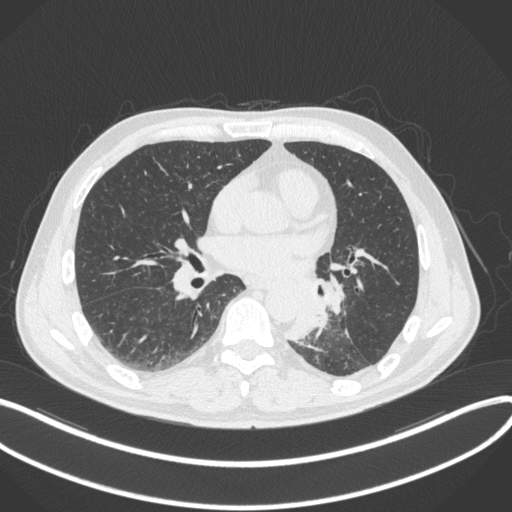
Chest CT, one axial slice. Slice 157 of 328 in the series (ordered by position). 120 kVp. Lung window (W 1500 / L -600 HU). 1 mm slice thickness. 512 × 512 image matrix. Male patient, age 59 years. From the clinical record (not read from this slice): clinical TNM (as recorded): T2a N2 M0.
Structures marked on this image (bounding box drawn by a radiologist):
- lung tumour (recorded histology: squamous cell carcinoma): bounding box [x1, y1, x2, y2] px = [284, 278, 350, 342]